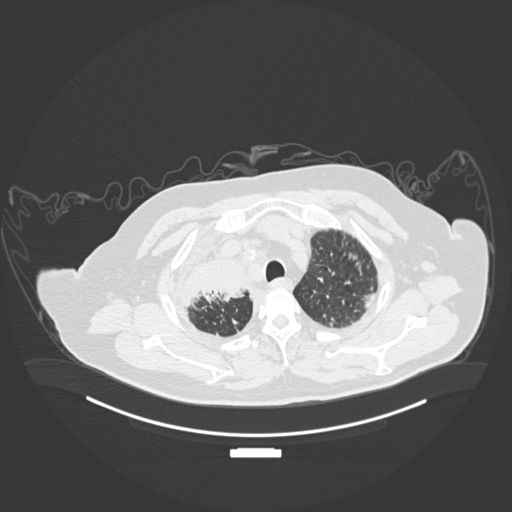
Chest CT, one axial slice; position 158 of 201 along the scan axis; reconstruction kernel B30f; lung window (W 1500 / L -600 HU); 512 × 512 image matrix. Patient: male, 69 years. From the clinical record (not read from this slice): clinical TNM (as recorded): T4 N3 M1.
Outlined on this slice (rectangle marked by the reading radiologist):
- lung tumour (recorded histology: adenocarcinoma): bounding box (x1, y1, x2, y2) in pixels: (176, 257, 247, 311)